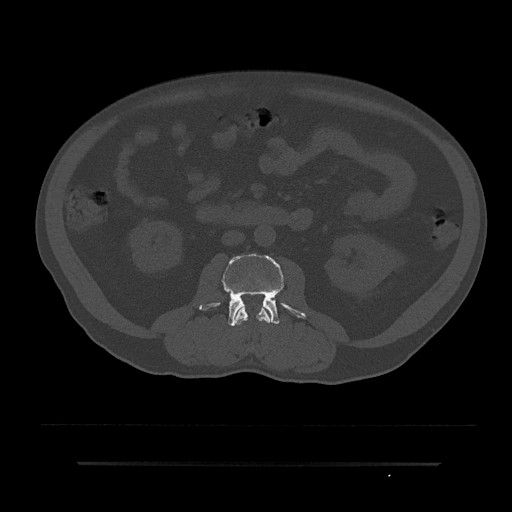
CT including the spine, one axial slice; slice 27 of 797 in the series (ordered by position); 120 kVp; bone window (W 1800 / L 400 HU); 0.5 mm slice thickness; 512 × 512 image matrix, field of view 464 × 464 mm. Patient: male, 59 years. Case-level facts recorded for this patient, not image findings: primary cancer: bile ducts.
Outlined on this slice (semi-automatically segmented with operator editing):
- L2 vertebra: bounding box (x1, y1, x2, y2) in pixels: (233, 306, 273, 325)
- L3 vertebra: (199, 253, 306, 326)